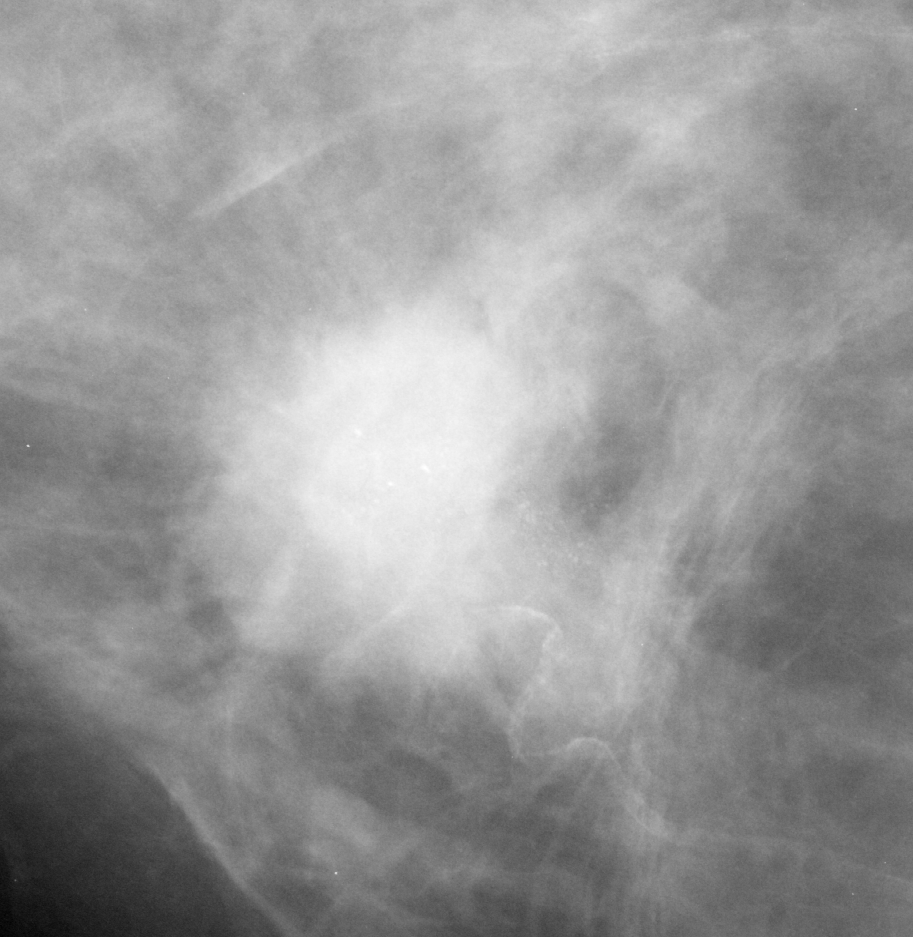
Cropped region of a digitized screen-film mammogram centred on a radiologist-marked abnormality; right breast; CC view; BI-RADS breast density category 3 (scale 1–4).
- Calcifications, morphology amorphous, distribution clustered; BI-RADS assessment category 5; subtlety rating 5 on a 1 (subtle) to 5 (obvious) scale; pathology result (as recorded, not read from the image): malignant.